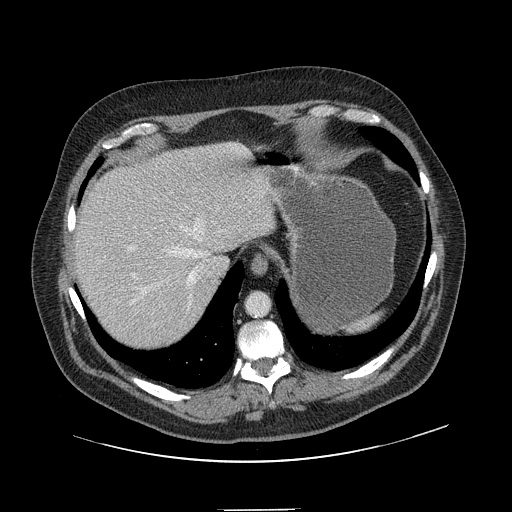
Contrast-enhanced abdominal CT, one axial slice. Slice 121 of 154 in the series (ordered by position). 120 kVp. Soft-tissue window (W 400 / L 40 HU). 512 × 512 image matrix, field of view 451 × 451 mm. Male patient, age 61 years. Case-level facts recorded for this patient, not image findings: diagnosis: colorectal cancer liver metastases, imaged before liver resection; multiple liver metastases: yes; largest metastasis: 2.6 cm; disease in both lobes: yes.
Outlined on this slice (manually delineated by an expert):
- hepatic veins: bounding box [x1, y1, x2, y2] px = [128, 215, 208, 304]
- liver: [74, 144, 275, 352]
- planned liver remnant (the part of the liver to remain after resection): [74, 144, 275, 349]
- portal vein (with intrahepatic branches): [131, 226, 136, 278]